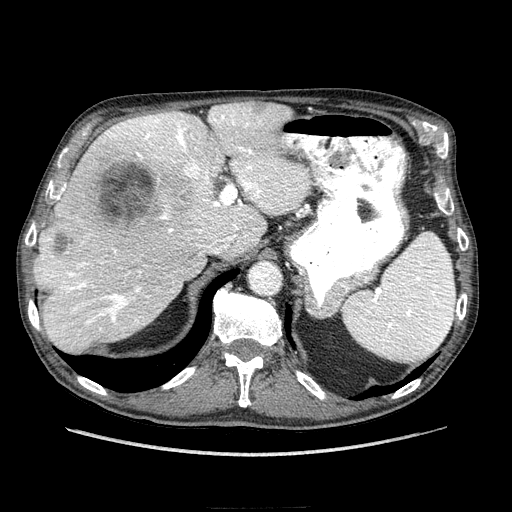
Contrast-enhanced abdominal CT (liver protocol), one axial slice. Position 163 of 218 along the scan axis. Reconstruction kernel STANDARD. Soft-tissue window (W 400 / L 40 HU). 2.5 mm slice thickness. 512 × 512 image matrix, field of view 380 × 380 mm. From the clinical record (not read from this slice): diagnosis: hepatocellular carcinoma (patient treated with transarterial chemoembolisation; whether this scan precedes or follows treatment is not stated here); TNM stage (as recorded): Stage-IIIA; Child-Pugh class: A; tumour differentiation: well differentiated; tumour size: 20 cm.
Outlined on this slice (semi-automatic segmentation, software-assisted and operator-edited):
- abdominal aorta: bounding box (x1, y1, x2, y2) in pixels: (251, 261, 281, 294)
- liver parenchyma outside the tumour (the mass and vessels are separate outlines, so this box may not span the whole liver): (34, 102, 305, 352)
- mass: (53, 110, 224, 252)
- liver vessels: (38, 106, 303, 334)